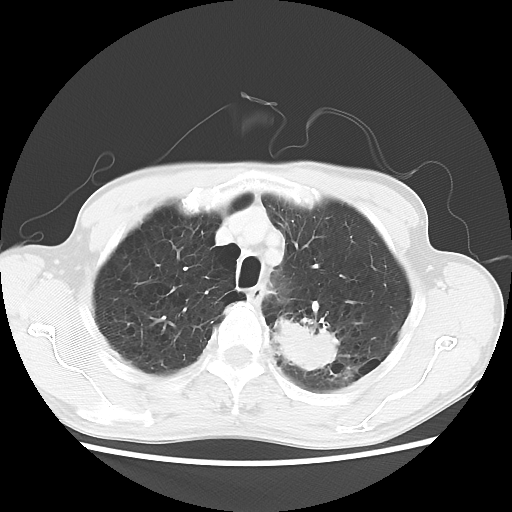
Chest CT, one axial slice; position 51 of 64 along the scan axis; lung window (W 1500 / L -600 HU); 512 × 512 image matrix, field of view 346 × 346 mm. Male patient, age 63 years. Case-level facts recorded for this patient, not image findings: clinical TNM (as recorded): T2 N0 M0.
Annotated regions visible in this slice (rectangle marked by the reading radiologist):
- lung tumour (recorded histology: adenocarcinoma): bounding box (x1, y1, x2, y2) in pixels: (271, 308, 341, 377)